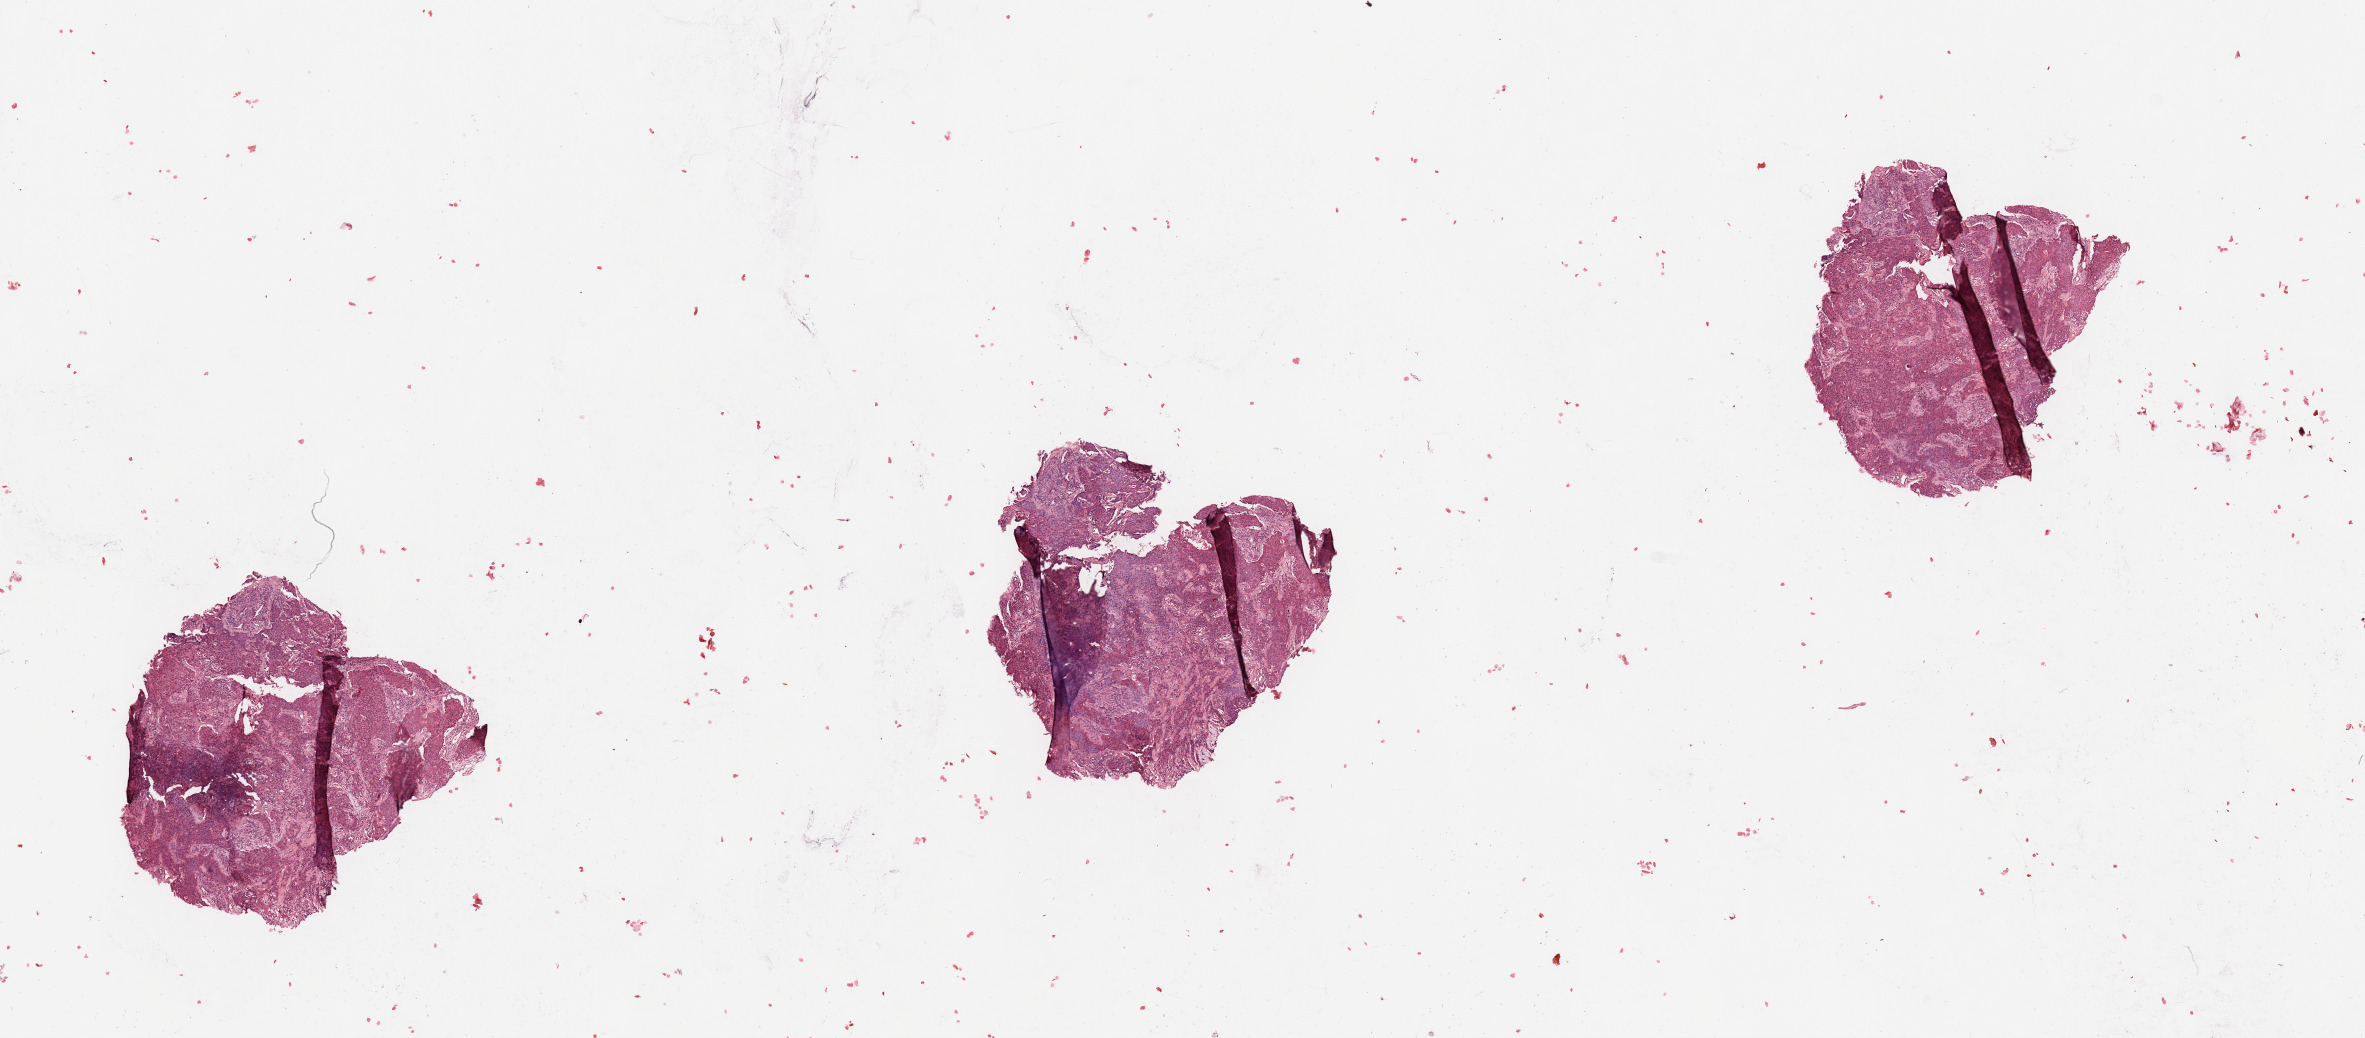
H&E-stained whole-slide image — a low-resolution overview of the entire scanned area, about 18.7 x 8.2 mm. Tumour tissue sample, sampled site: larynx. Patient: female, age 53 years. Histologic grade: G2 (moderately differentiated). Composition of this section per pathologist review: tumour nuclei 80%, necrosis 3%.
• diagnosis: Squamous cell carcinoma, NOS (larynx, NOS)
• AJCC pathologic stage: III
• primary tumour site (as recorded): larynx